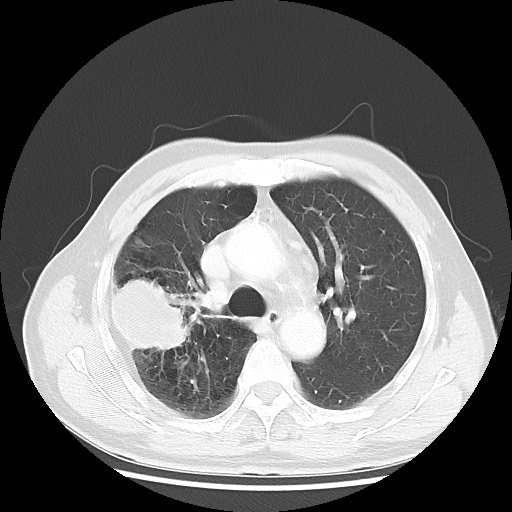
Chest CT, one axial slice; position 34 of 50 along the scan axis; lung window (W 1500 / L -600 HU); 5 mm slice thickness; 512 × 512 image matrix. Male patient, age 69 years. From the clinical record (not read from this slice): clinical TNM (as recorded): T3 N0 M0.
Annotated regions visible in this slice (bounding box drawn by a radiologist):
- lung tumour (recorded histology: adenocarcinoma): box from (x=112, y=271) to (x=192, y=357) px